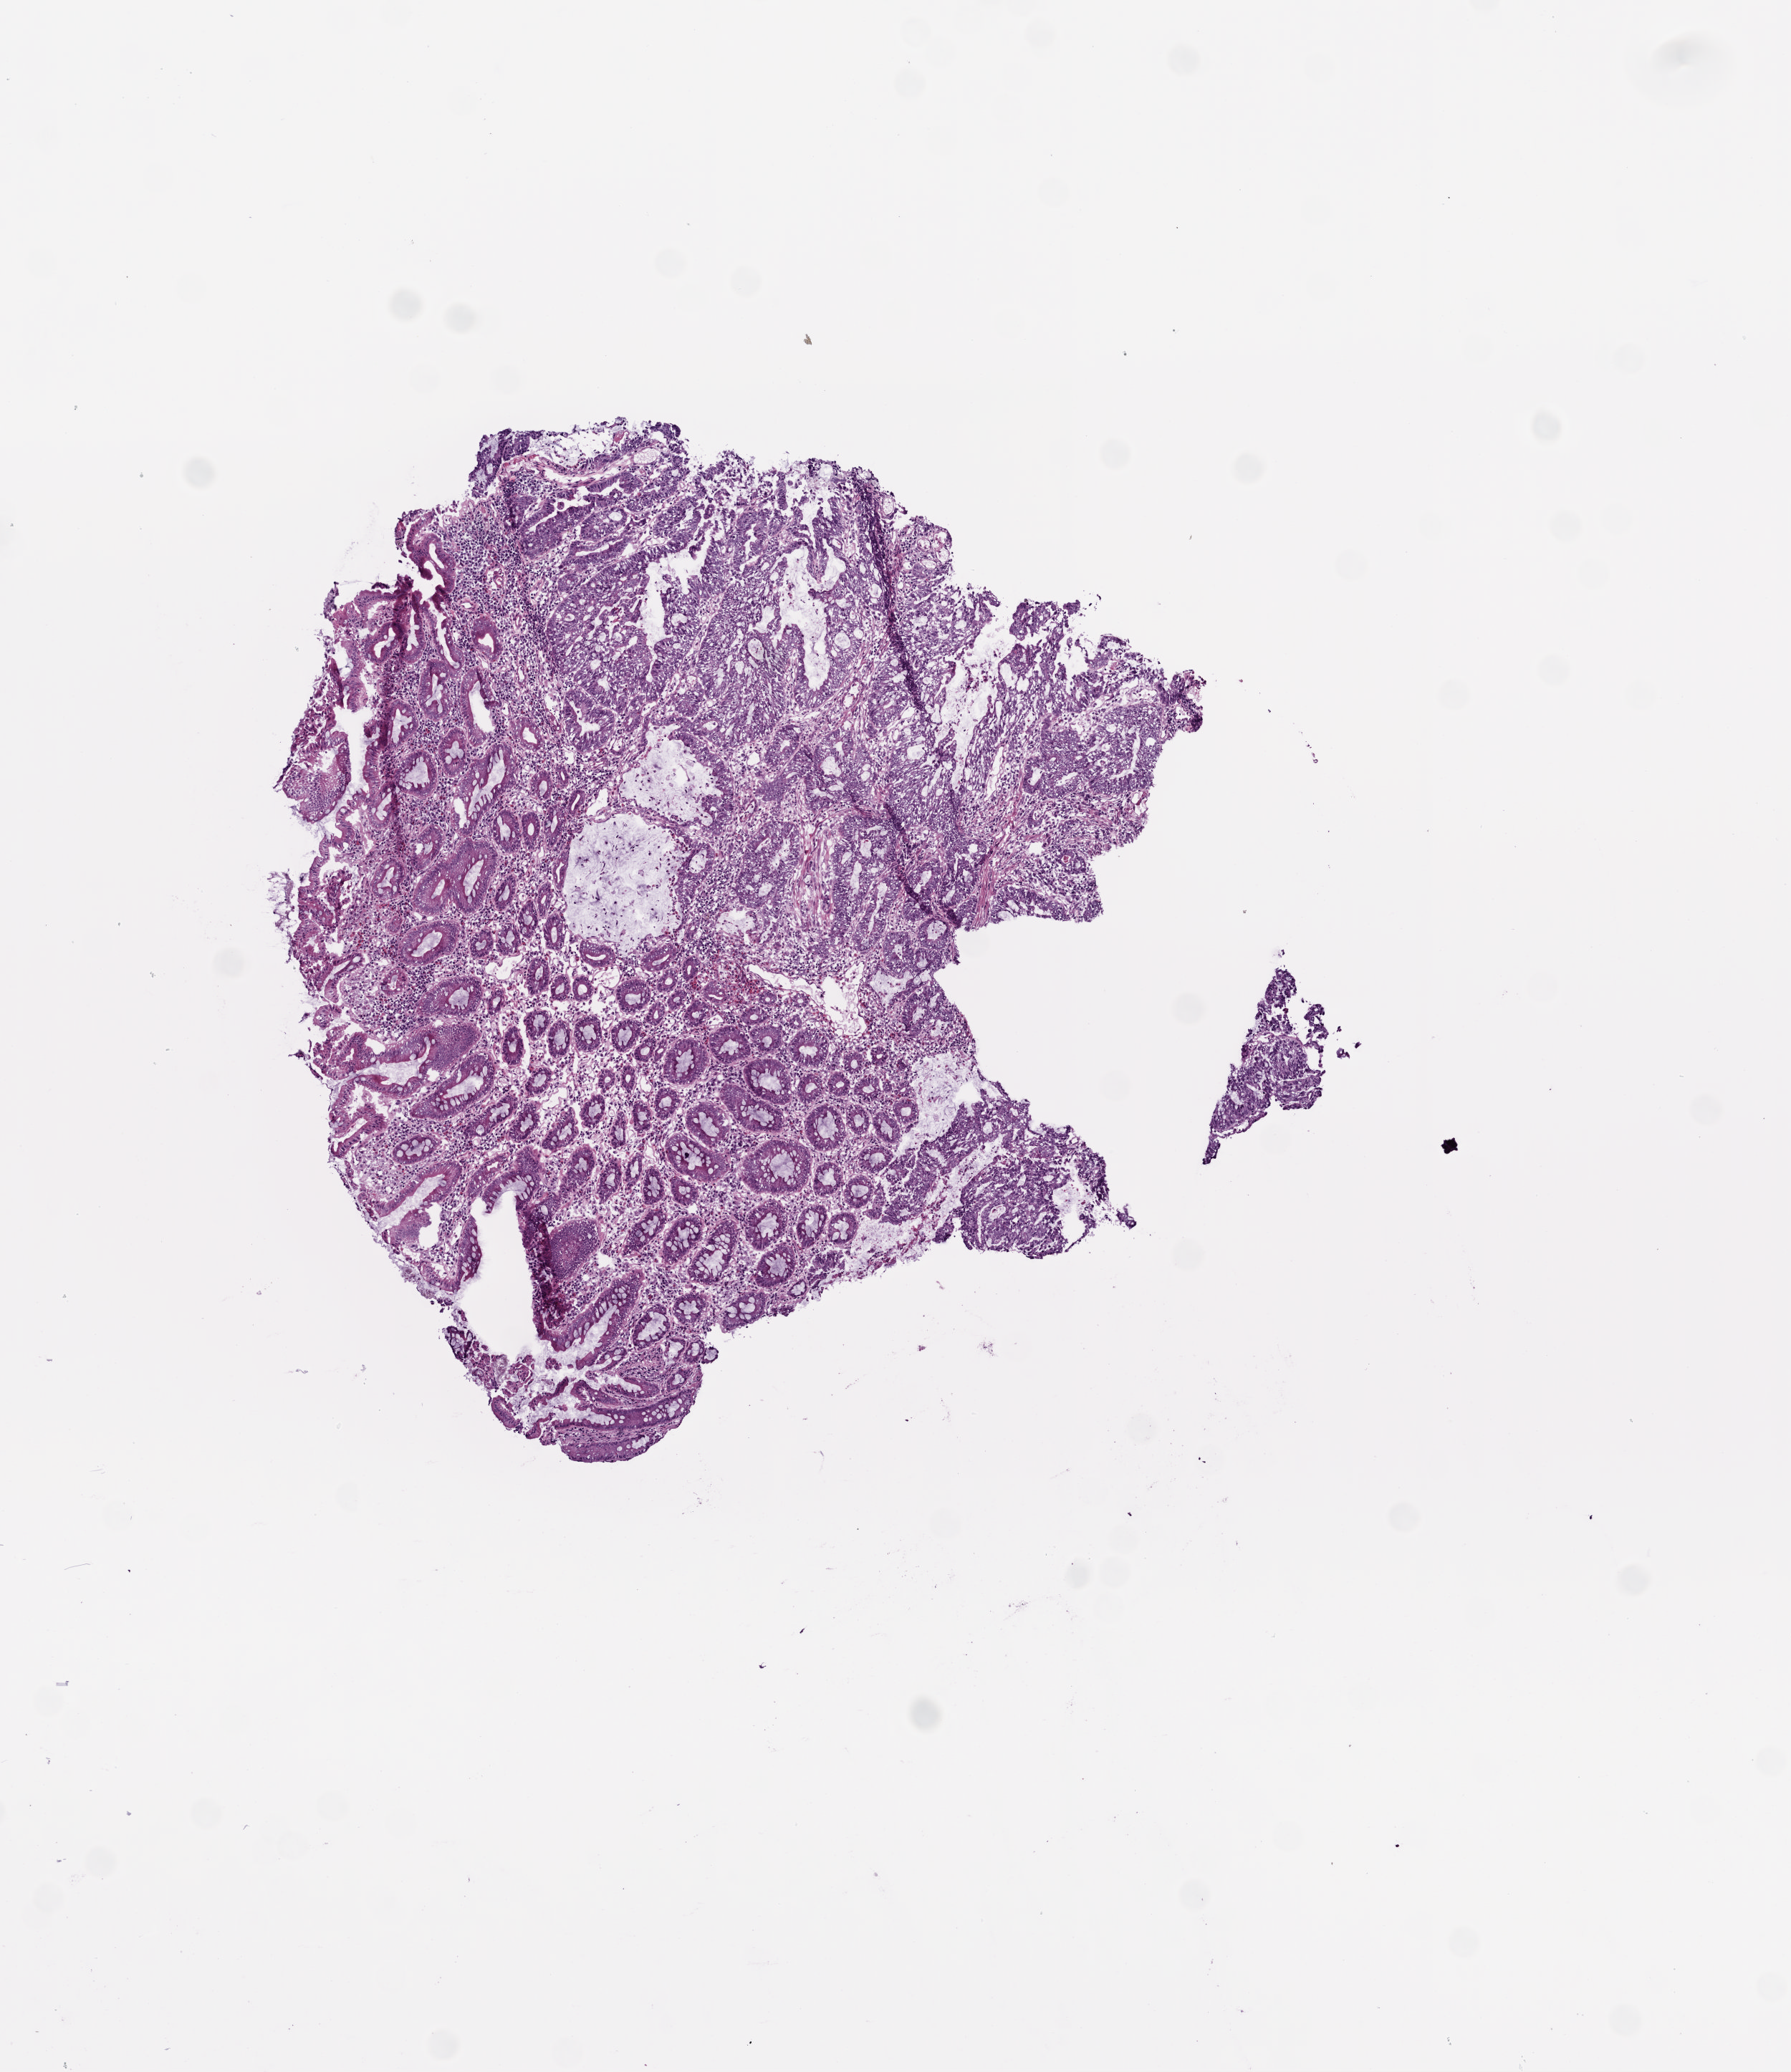
H&E whole-slide image, a low-resolution overview of the entire scanned area, about 5.0 x 5.8 mm (from a 20x scan), frozen section from the bottom of the tissue portion, primary tumour sample from the colon. Female patient; age at initial diagnosis 68 years. Pathologist review of this section (percent, as recorded): tumour cells 27%, tumour nuclei 50%, normal cells 55%, stromal cells 15%, necrosis 3%.
AJCC pathologic stage: IIIB (6th edition). Diagnosis: Mucinous adenocarcinoma (cecum). Lymph nodes positive (case pathology): 1 of 18 examined.